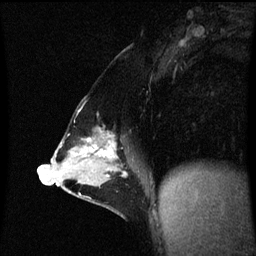
Breast MRI (dynamic contrast-enhanced), one sagittal slice. Slice 30 of 60 in the series (ordered by position). Dynamic contrast-enhanced series, image 2 of 3 at this slice position (ordered by acquisition). 1.5 T. TE 4.2 ms, TR 8.9 ms. 2 mm slice thickness. 256 × 256 image matrix, field of view 200 × 200 mm. Patient: female, 47 years. From the clinical record (not read from this slice): setting: breast cancer imaged before/during neoadjuvant chemotherapy; receptor status: HR-positive, HER2-negative.
Outlined on this slice (semi-automatically segmented with operator editing):
- analysis volume of interest (the breast-tissue region the enhancement analysis was run in; not a lesion): bounding box (x1, y1, x2, y2) in pixels: (53, 128, 130, 209)
- tumour enhancement mask (voxels above the 70 % enhancement threshold inside the analysis volume of interest): (58, 132, 128, 185)